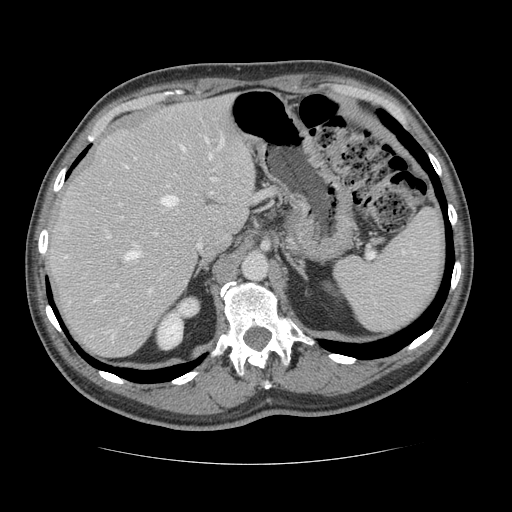
Contrast-enhanced abdominal CT, one axial slice. Reconstruction kernel STANDARD. Soft-tissue window (W 400 / L 40 HU). 512 × 512 image matrix, field of view 377 × 377 mm. Male patient, age 68 years. From the clinical record (not read from this slice): diagnosis: colorectal cancer liver metastases, imaged before liver resection.
Outlined on this slice (expert manual segmentation):
- hepatic veins: bounding box <112,137,223,338> (left, top, right, bottom; pixels)
- liver: <47,97,256,359>
- planned liver remnant (the part of the liver to remain after resection): <47,97,256,336>
- portal vein (with intrahepatic branches): <107,141,217,292>